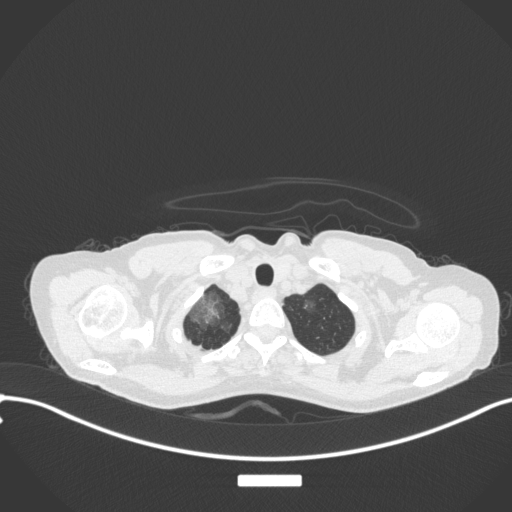
Chest CT, one axial slice; position 306 of 311 along the scan axis; reconstruction kernel B31f; 120 kVp; lung window (W 1500 / L -600 HU); 512 × 512 image matrix, field of view 400 × 400 mm. Female patient, age 59 years. Case-level facts recorded for this patient, not image findings: clinical TNM (as recorded): T3 N0 M0; histopathological grade: G1.
Structures marked on this image (rectangle marked by the reading radiologist):
- lung tumour (recorded histology: adenocarcinoma): box from (x=182, y=285) to (x=223, y=327) px